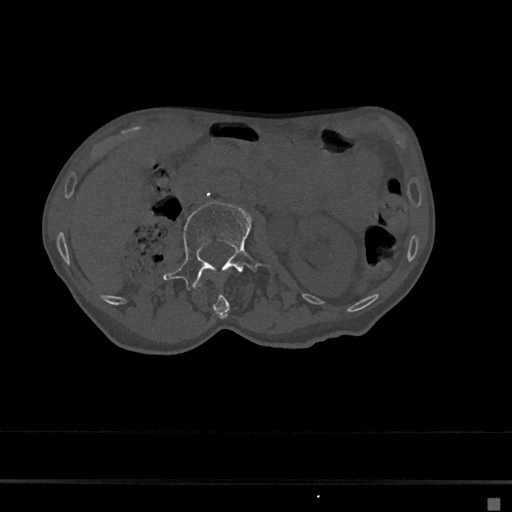
CT including the spine, one axial slice. Position 21 of 797 along the scan axis. Bone window (W 1800 / L 400 HU). 0.5 mm slice thickness. 512 × 512 image matrix, field of view 360 × 360 mm. Patient: female, 68 years. From the clinical record (not read from this slice): primary cancer: renal.
Outlined on this slice (semi-automatically segmented with operator editing):
- L1 vertebra: box from (x=198, y=278) to (x=229, y=319) px
- L2 vertebra: (x=163, y=202)–(x=270, y=291)